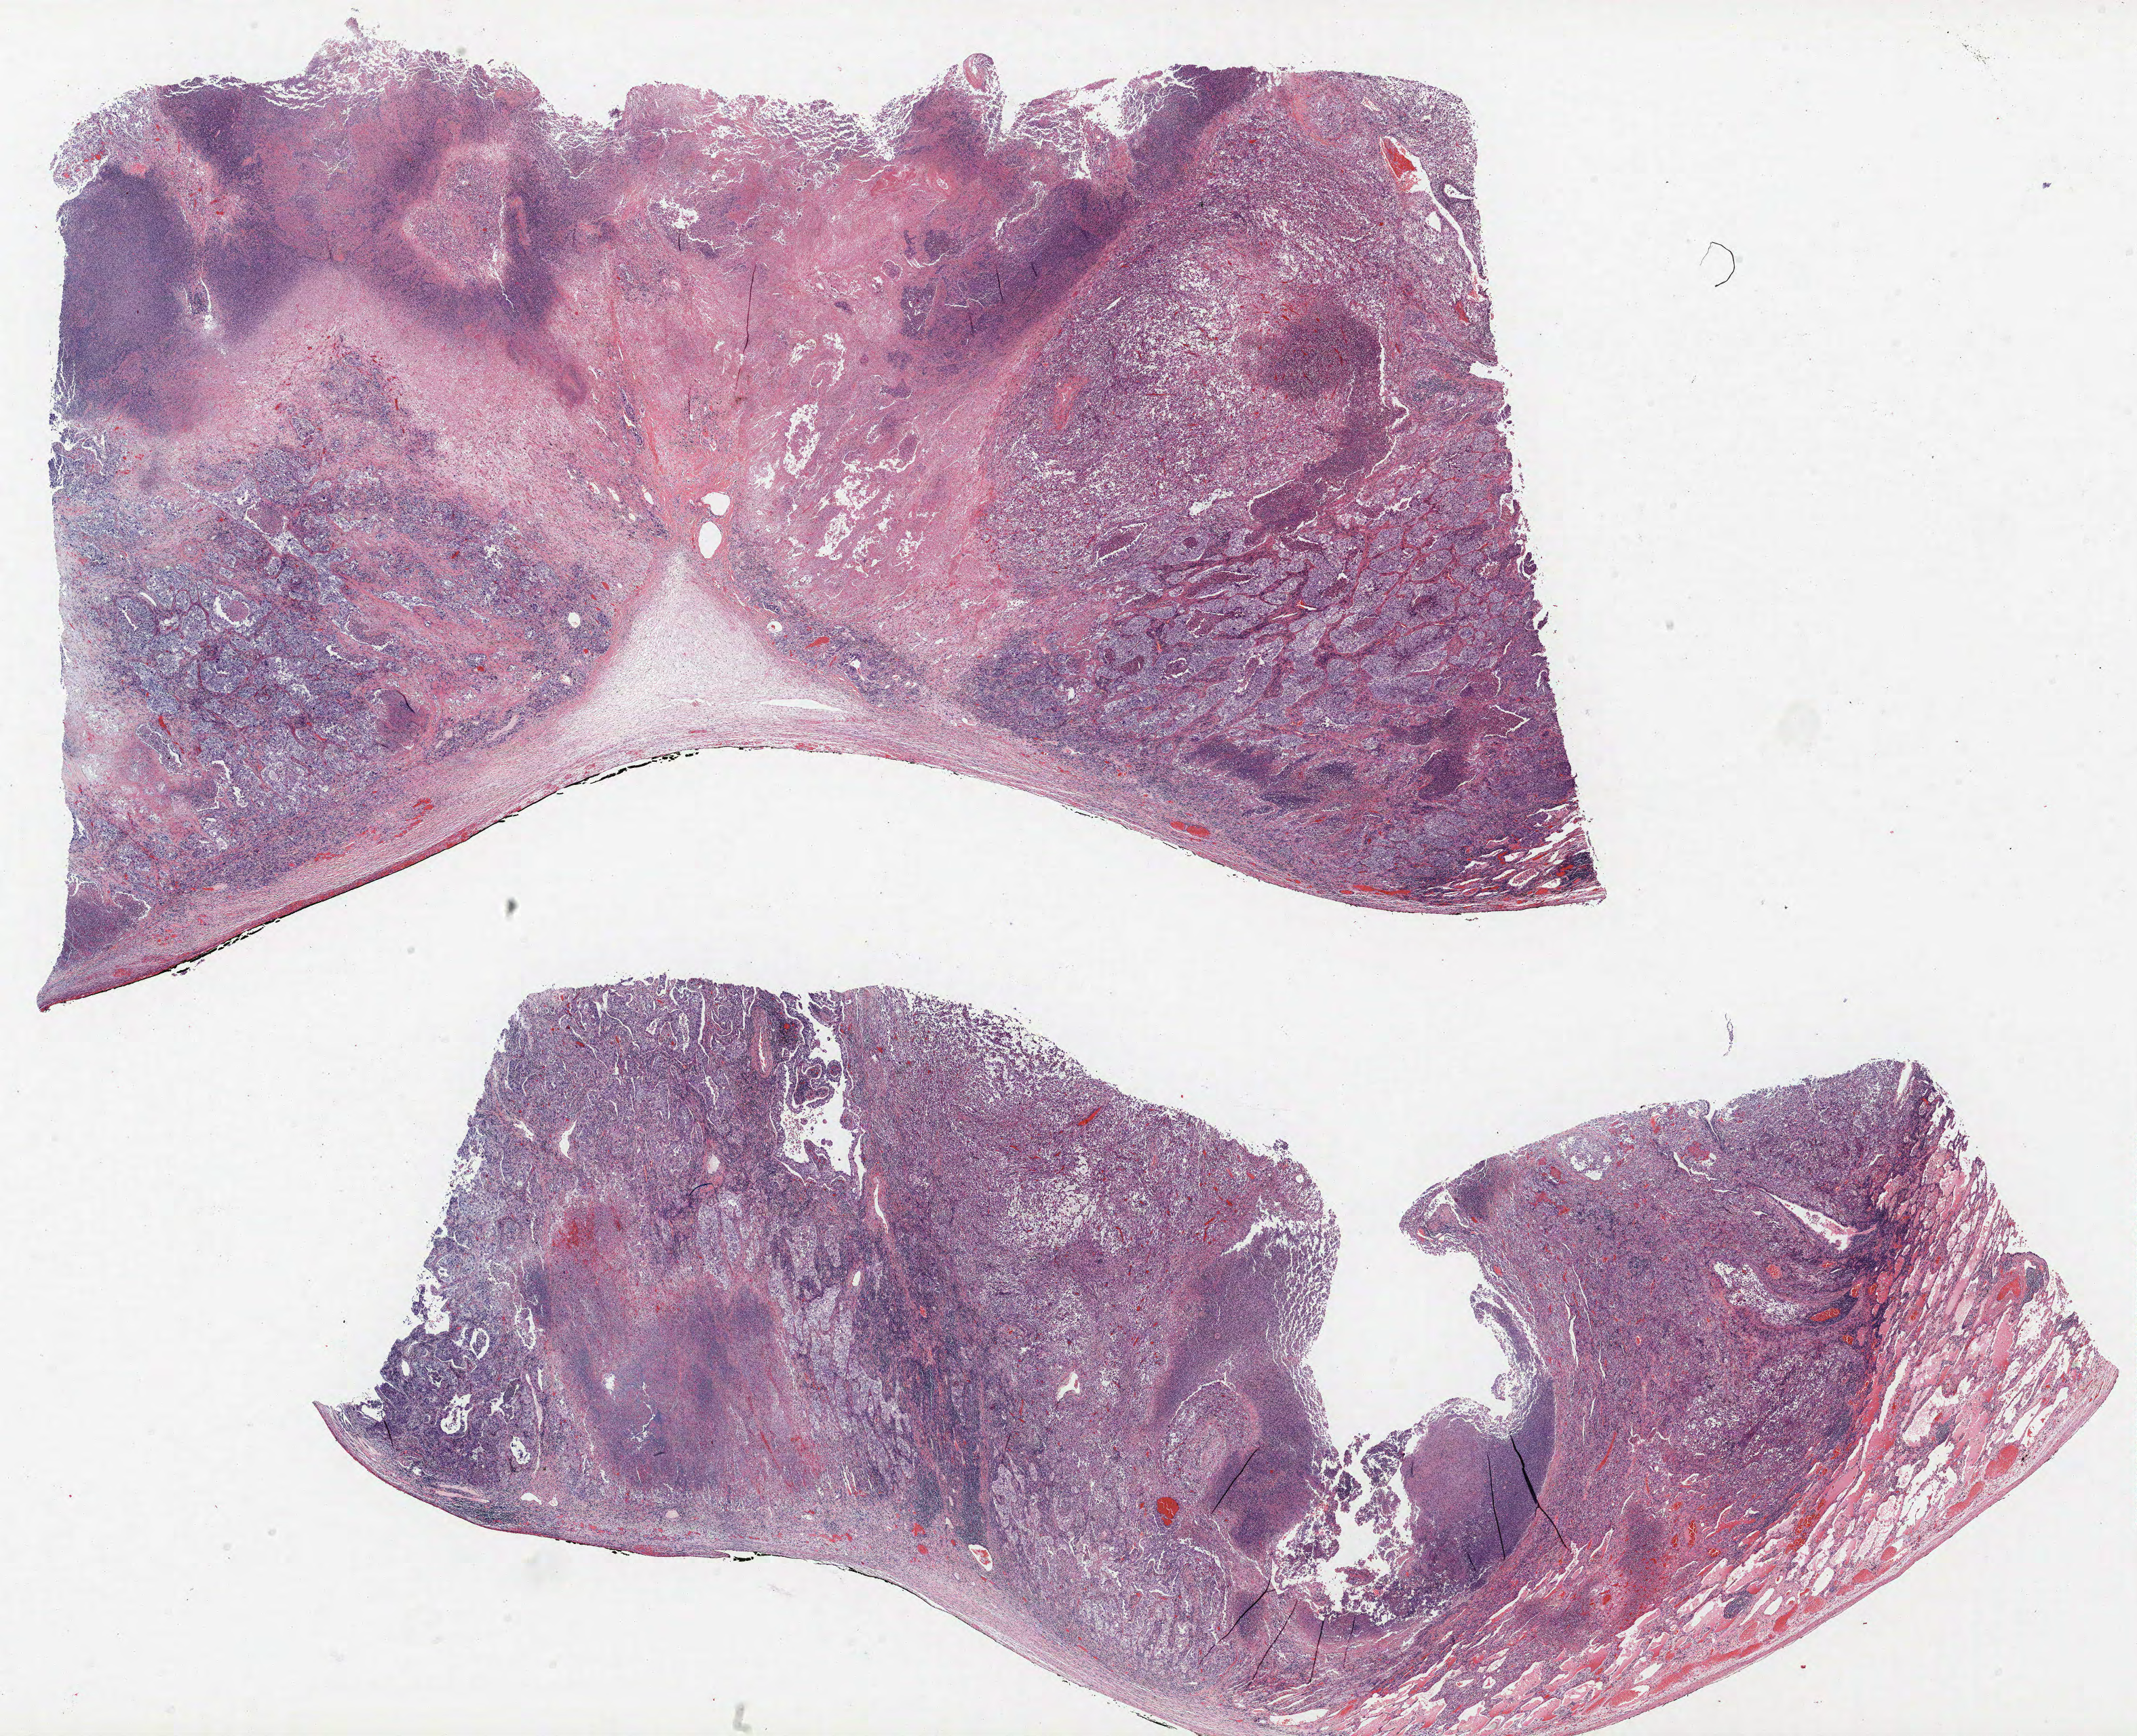
Hematoxylin and eosin (H&E) stained whole-slide image — low-resolution overview of the scanned area, about 25.2 x 20.5 mm (from a 40x scan). FFPE section. Lung tissue. Female, age 56 at enrolment. Current smoker at enrolment. Grade: poorly differentiated (G3).
- stage (AJCC 6th edition): IIB
- participant's lung-cancer diagnosis: Adenocarcinoma, NOS (ICD-O-3 8140/3)
- ICD-O-3 topography: lower lobe of lung (C34.3)
- tumour size (pathology): 60 mm
- primary tumour location (clinical record): right lower lobe